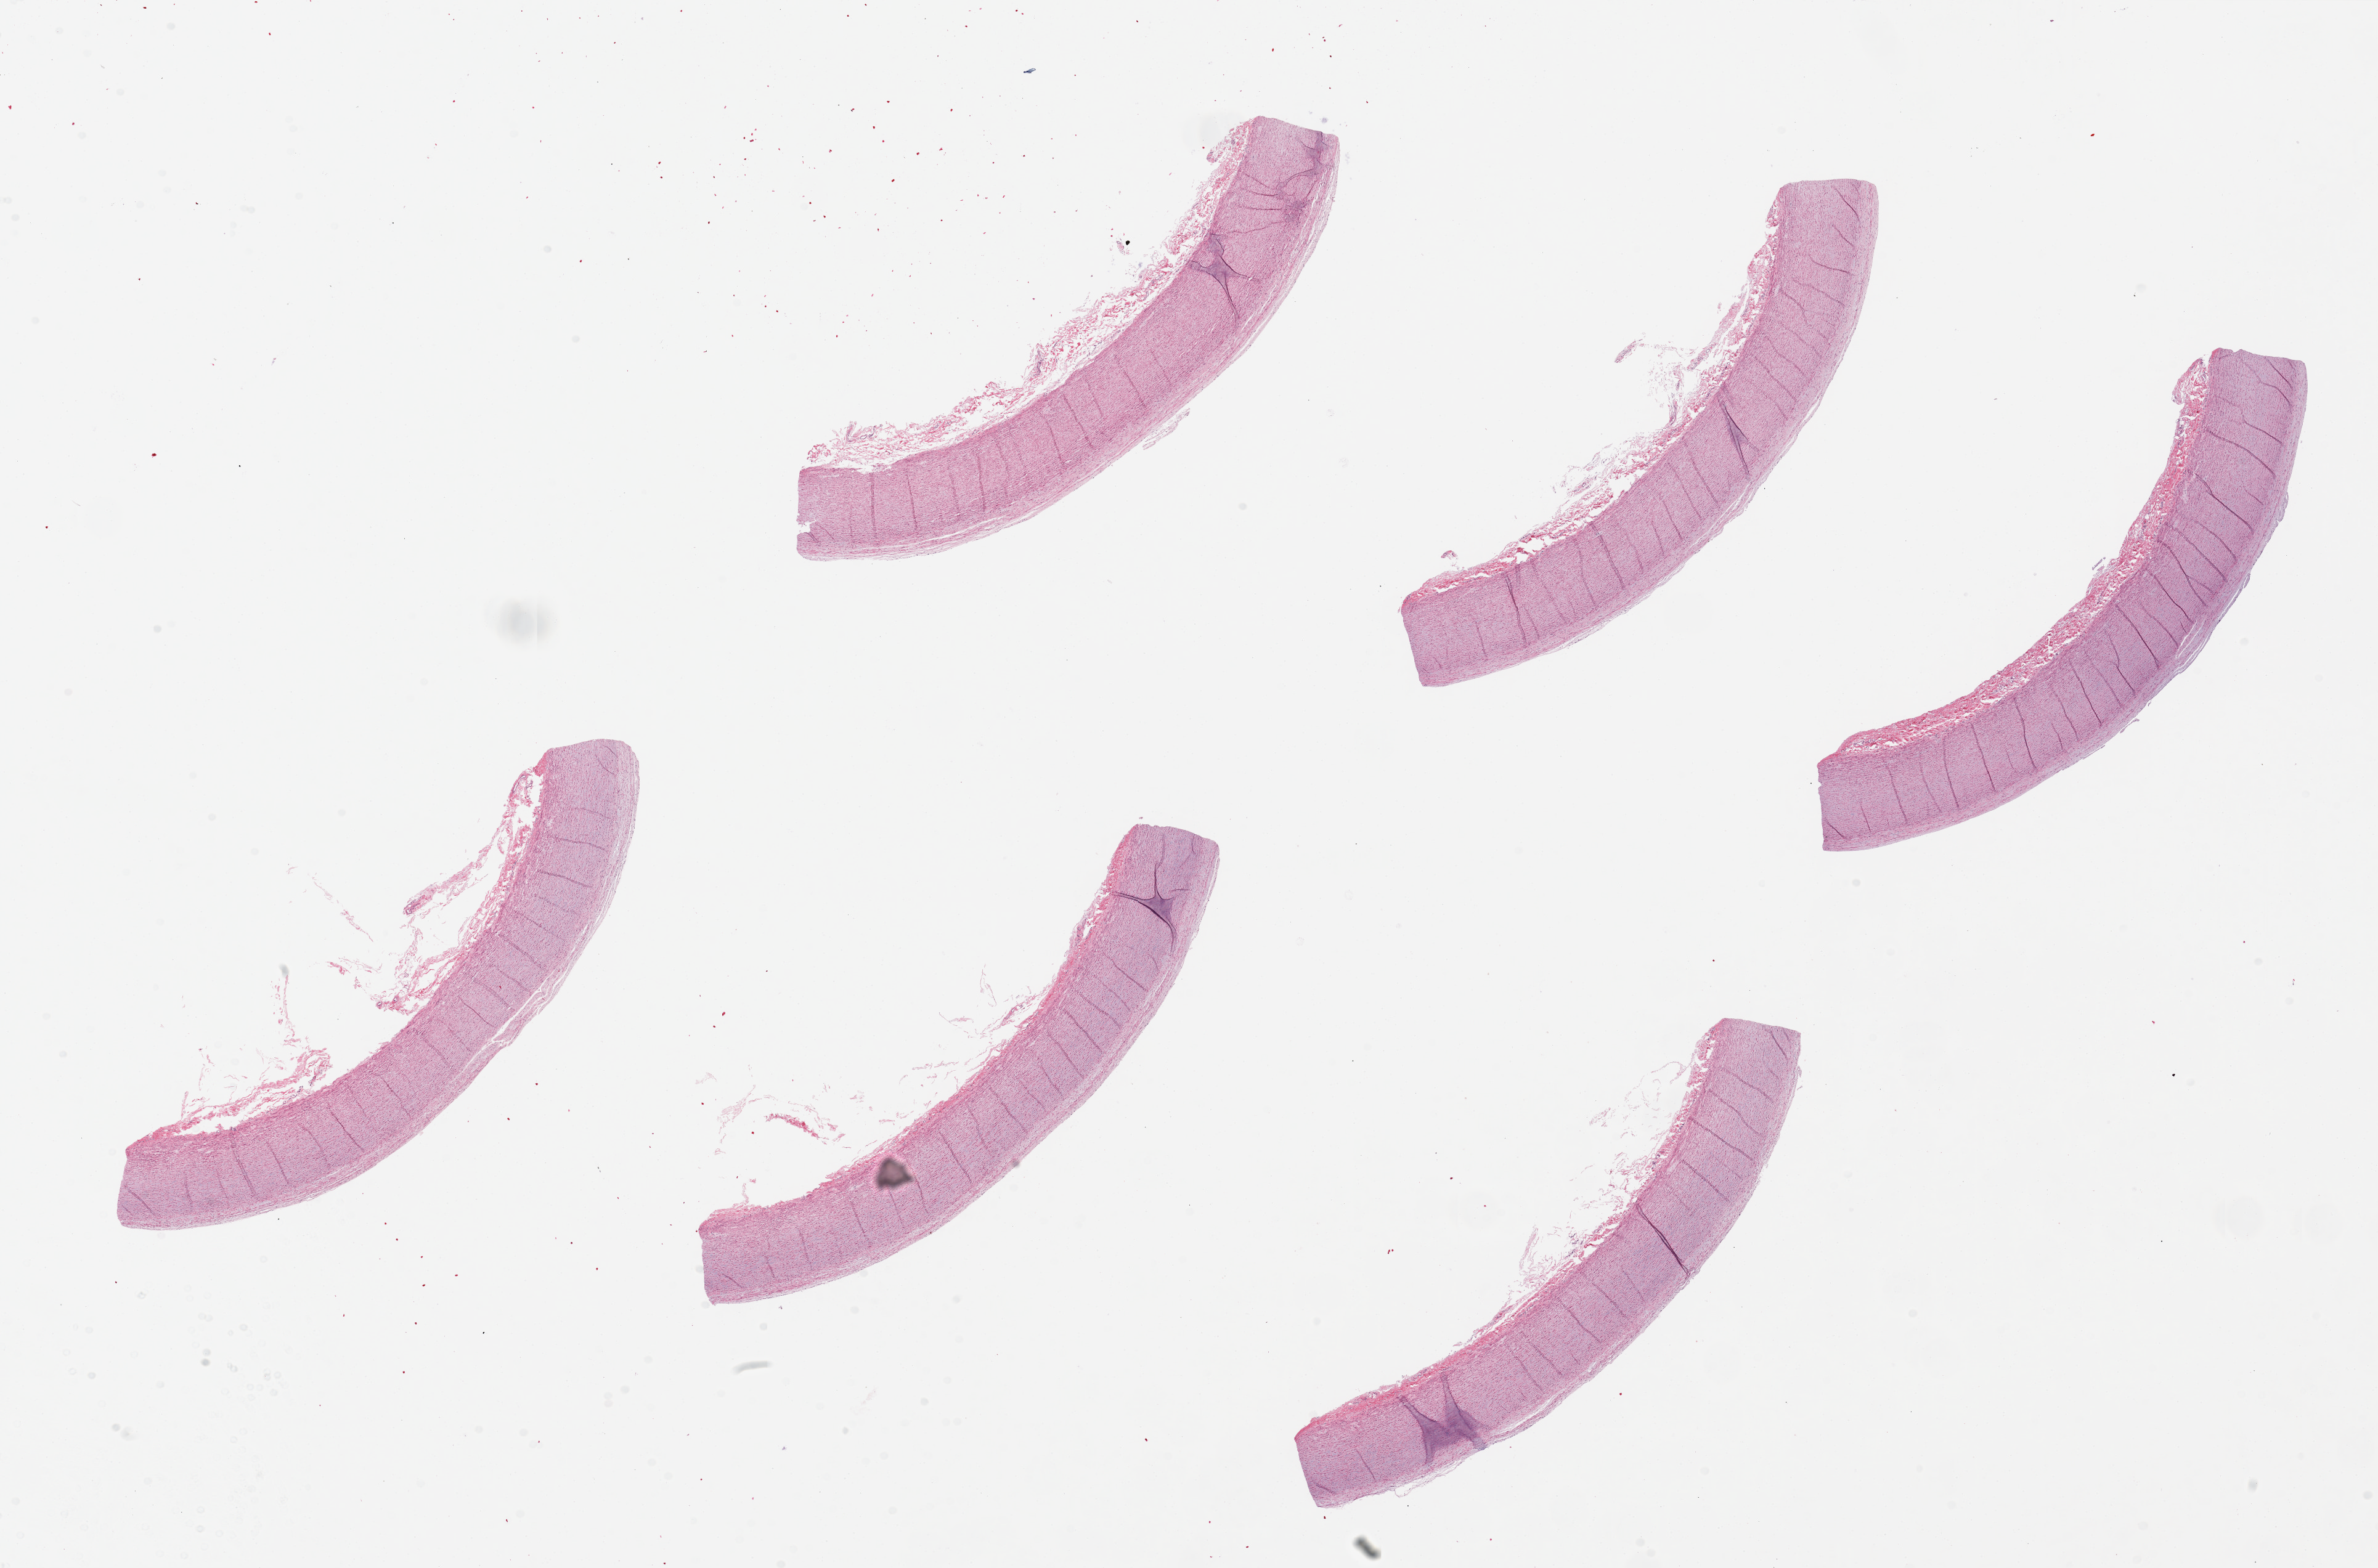
H&E whole-slide image — whole scanned area (about 30.5 x 20.1 mm, slide scanned at 20x) shown as a low-resolution overview, PAXgene-fixed paraffin-embedded (PFPE) section, sampled site (target tissue): aorta, donor tissue sample. Female donor.
Reviewer comment on this tissue sample: 6 pieces, up to 9x4mm.